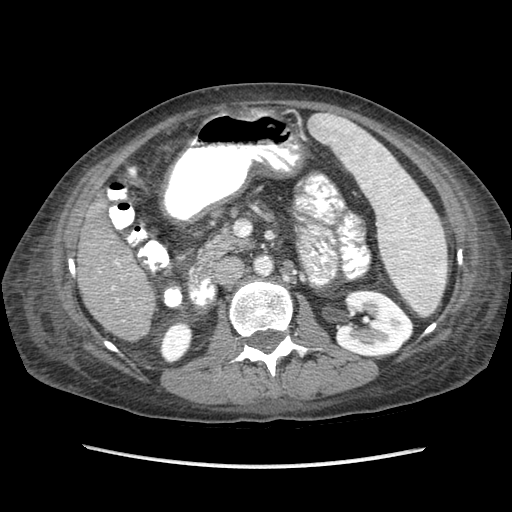
Contrast-enhanced abdominal CT (liver protocol), one axial slice. Slice 27 of 87 in the series (ordered by position). Soft-tissue window (W 400 / L 40 HU). 2.5 mm slice thickness. 512 × 512 image matrix, field of view 340 × 340 mm. From the clinical record (not read from this slice): diagnosis: hepatocellular carcinoma (patient treated with transarterial chemoembolisation; whether this scan precedes or follows treatment is not stated here); TNM stage (as recorded): Stage-IIIB; Child-Pugh class: A; tumour differentiation: no biopsy; tumour nodularity: uninodular.
Outlined on this slice (semi-automatic segmentation, software-assisted and operator-edited):
- liver parenchyma outside the tumour (the mass and vessels are separate outlines, so this box may not span the whole liver): bounding box (x1, y1, x2, y2) in pixels: (78, 198, 154, 340)
- liver vessels: (112, 260, 121, 302)